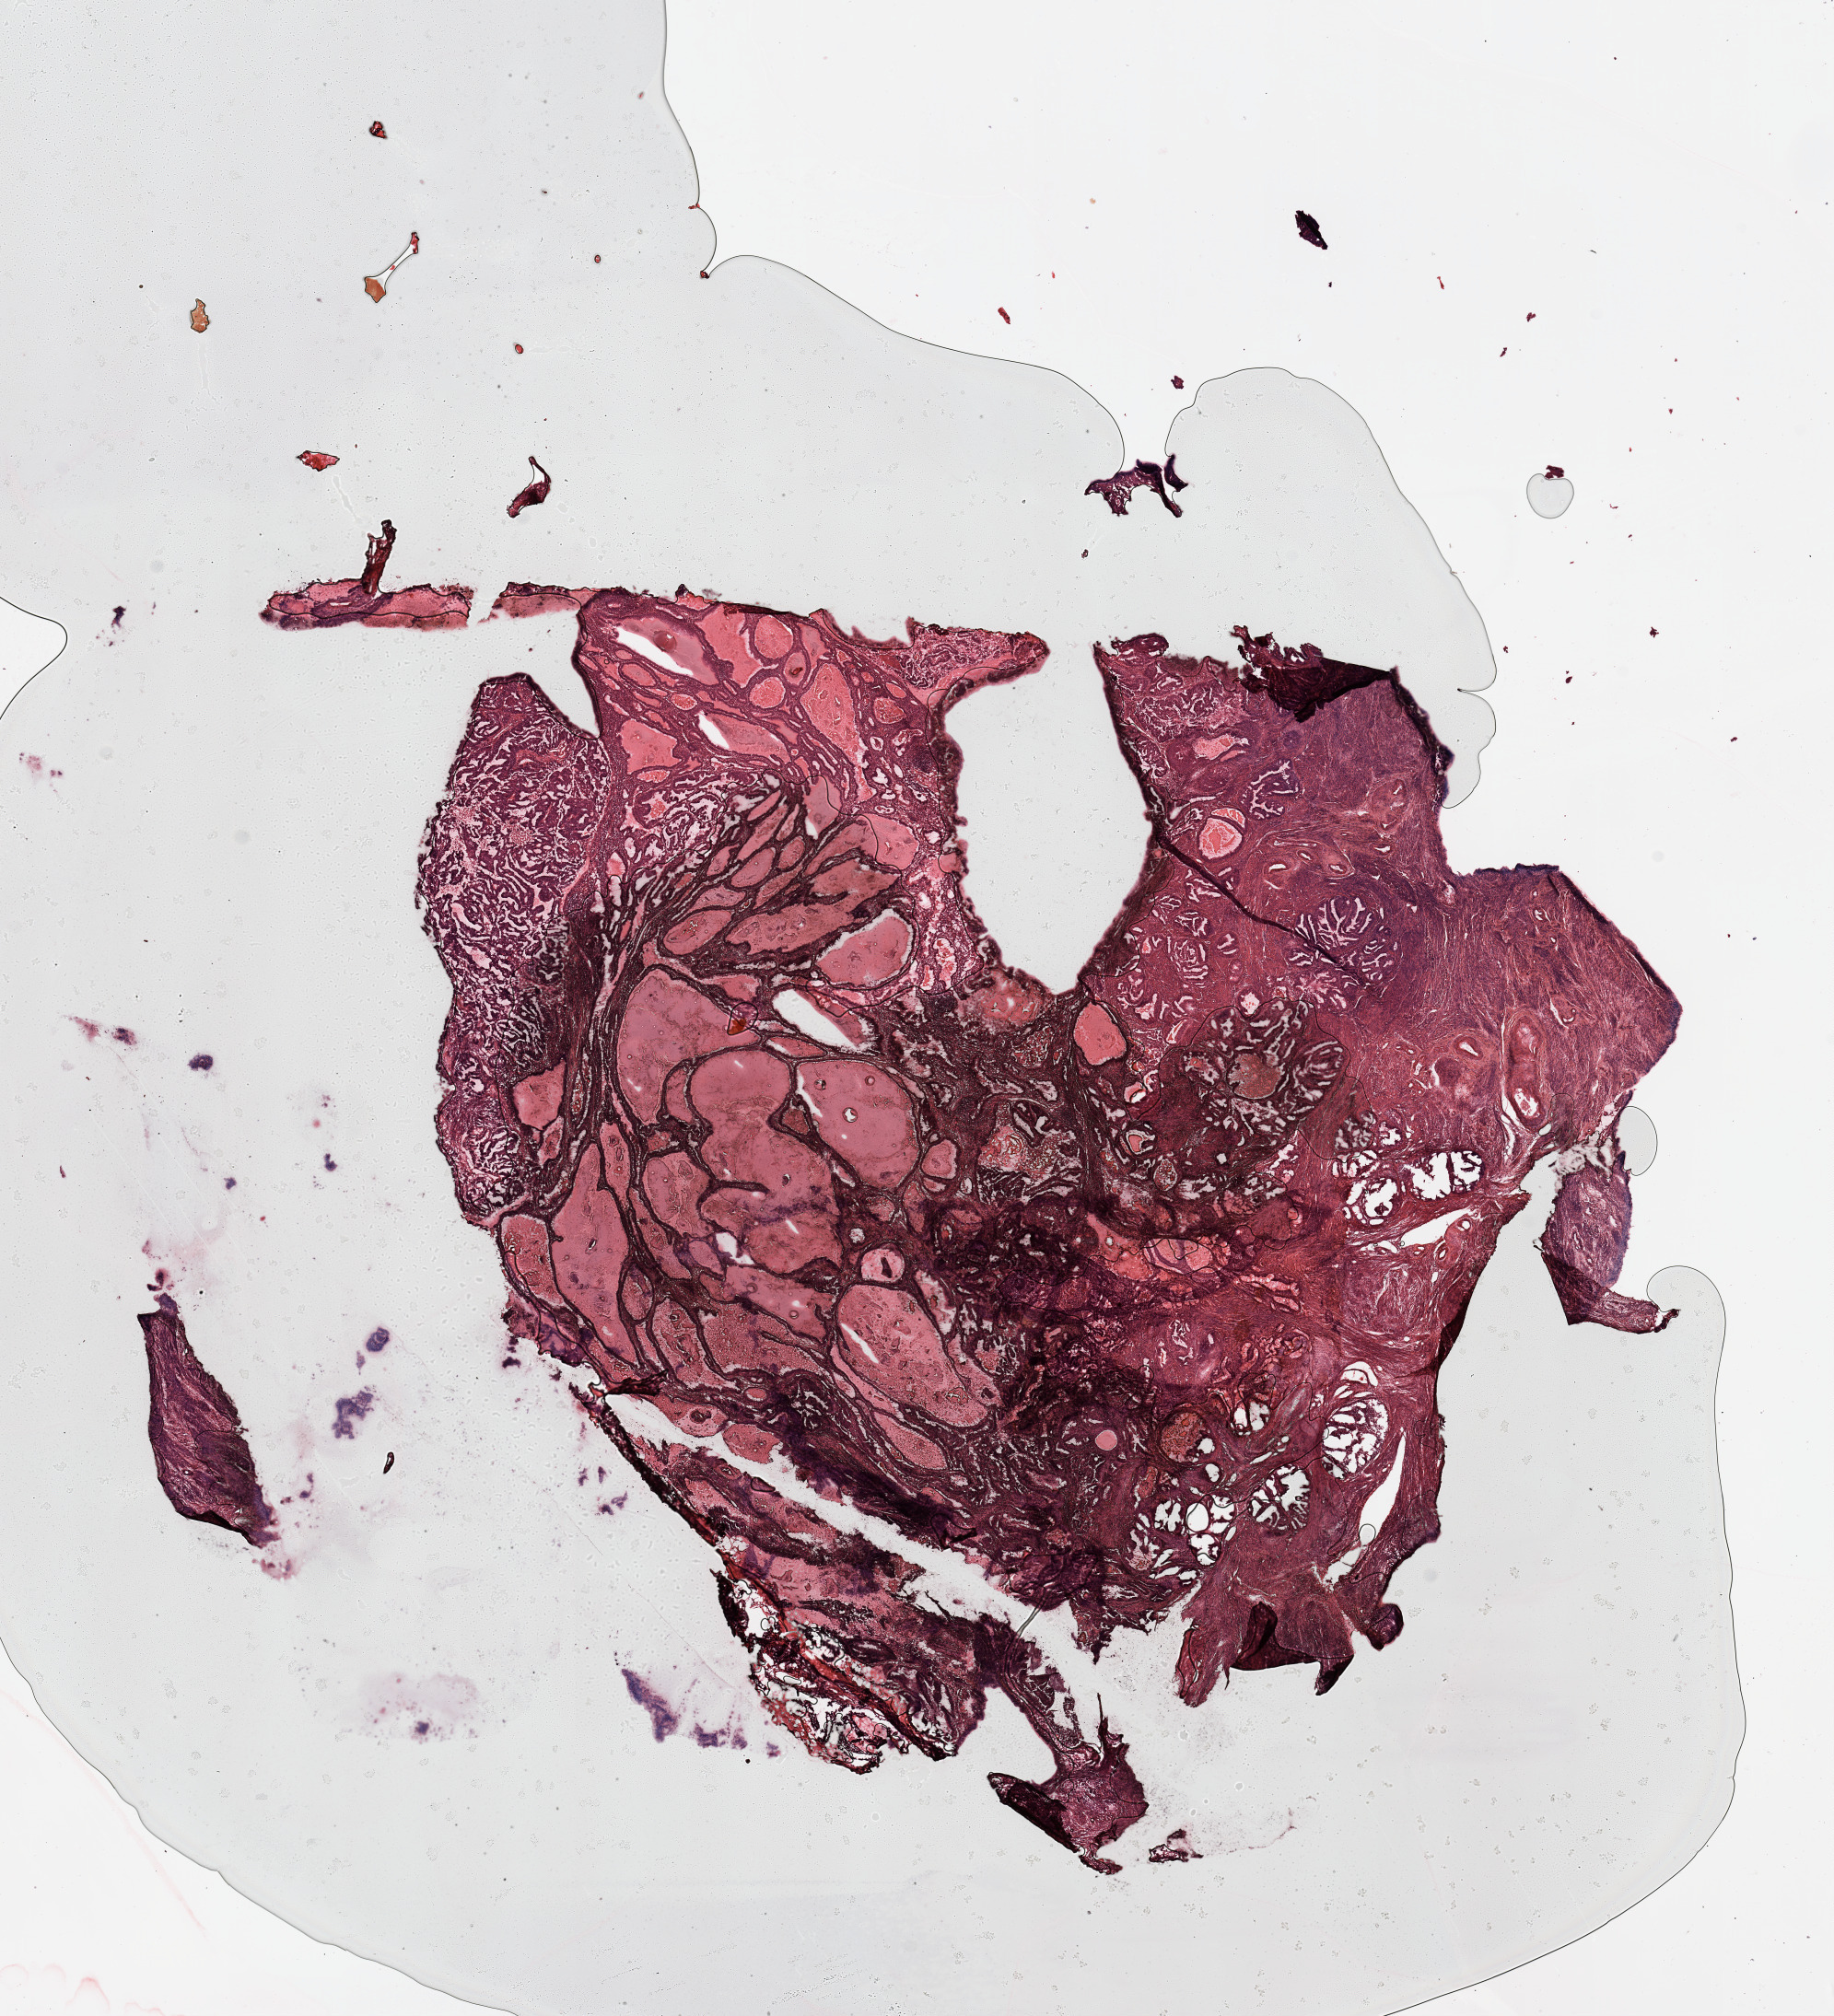
H&E-stained whole-slide image — whole scanned area (about 15.8 x 17.3 mm, acquisition: 20x scan) shown as a low-resolution overview, tumour tissue sample, uterus. Female, 70 y/o.
Diagnosis: Endometrioid adenocarcinoma, NOS.